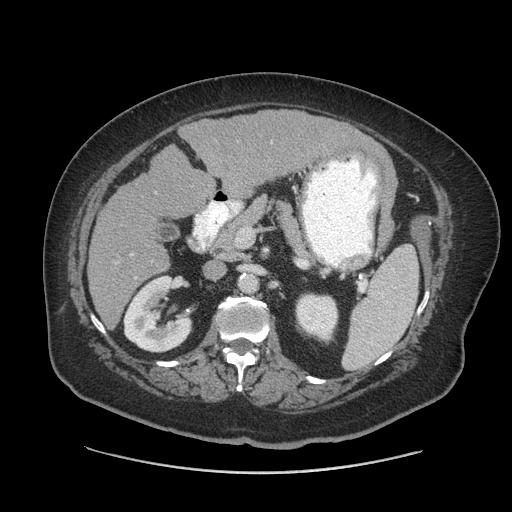
Contrast-enhanced abdominal CT (liver protocol), one axial slice; slice 33 of 91 in the series (ordered by position); reconstruction kernel STANDARD; soft-tissue window (W 400 / L 40 HU); 2.5 mm slice thickness; 512 × 512 image matrix, field of view 420 × 420 mm. Case-level facts recorded for this patient, not image findings: diagnosis: hepatocellular carcinoma (patient treated with transarterial chemoembolisation; whether this scan precedes or follows treatment is not stated here); TNM stage (as recorded): Stage-I; Child-Pugh class: A; tumour differentiation: well differentiated; tumour nodularity: uninodular.
Structures marked on this image (semi-automatic segmentation, software-assisted and operator-edited):
- liver parenchyma outside the tumour (the mass and vessels are separate outlines, so this box may not span the whole liver): bounding box <88,110,382,328> (left, top, right, bottom; pixels)